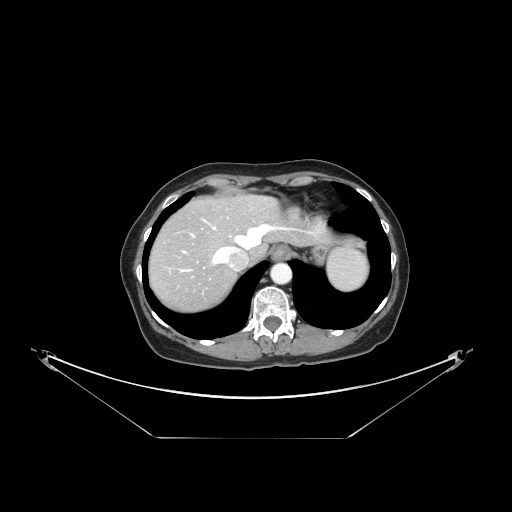
Contrast-enhanced abdominal CT, one axial slice; position 125 of 148 along the scan axis; reconstruction kernel STANDARD; 120 kVp; intravenous contrast given; soft-tissue window (W 400 / L 40 HU); 2.5 mm slice thickness; 512 × 512 image matrix, field of view 500 × 500 mm. Female patient, age 73 years. From the clinical record (not read from this slice): diagnosis: colorectal cancer liver metastases, imaged before liver resection.
Outlined on this slice (expert manual segmentation):
- hepatic veins: bounding box (x1, y1, x2, y2) in pixels: (183, 221, 295, 271)
- liver: (150, 197, 322, 310)
- planned liver remnant (the part of the liver to remain after resection): (178, 197, 319, 257)